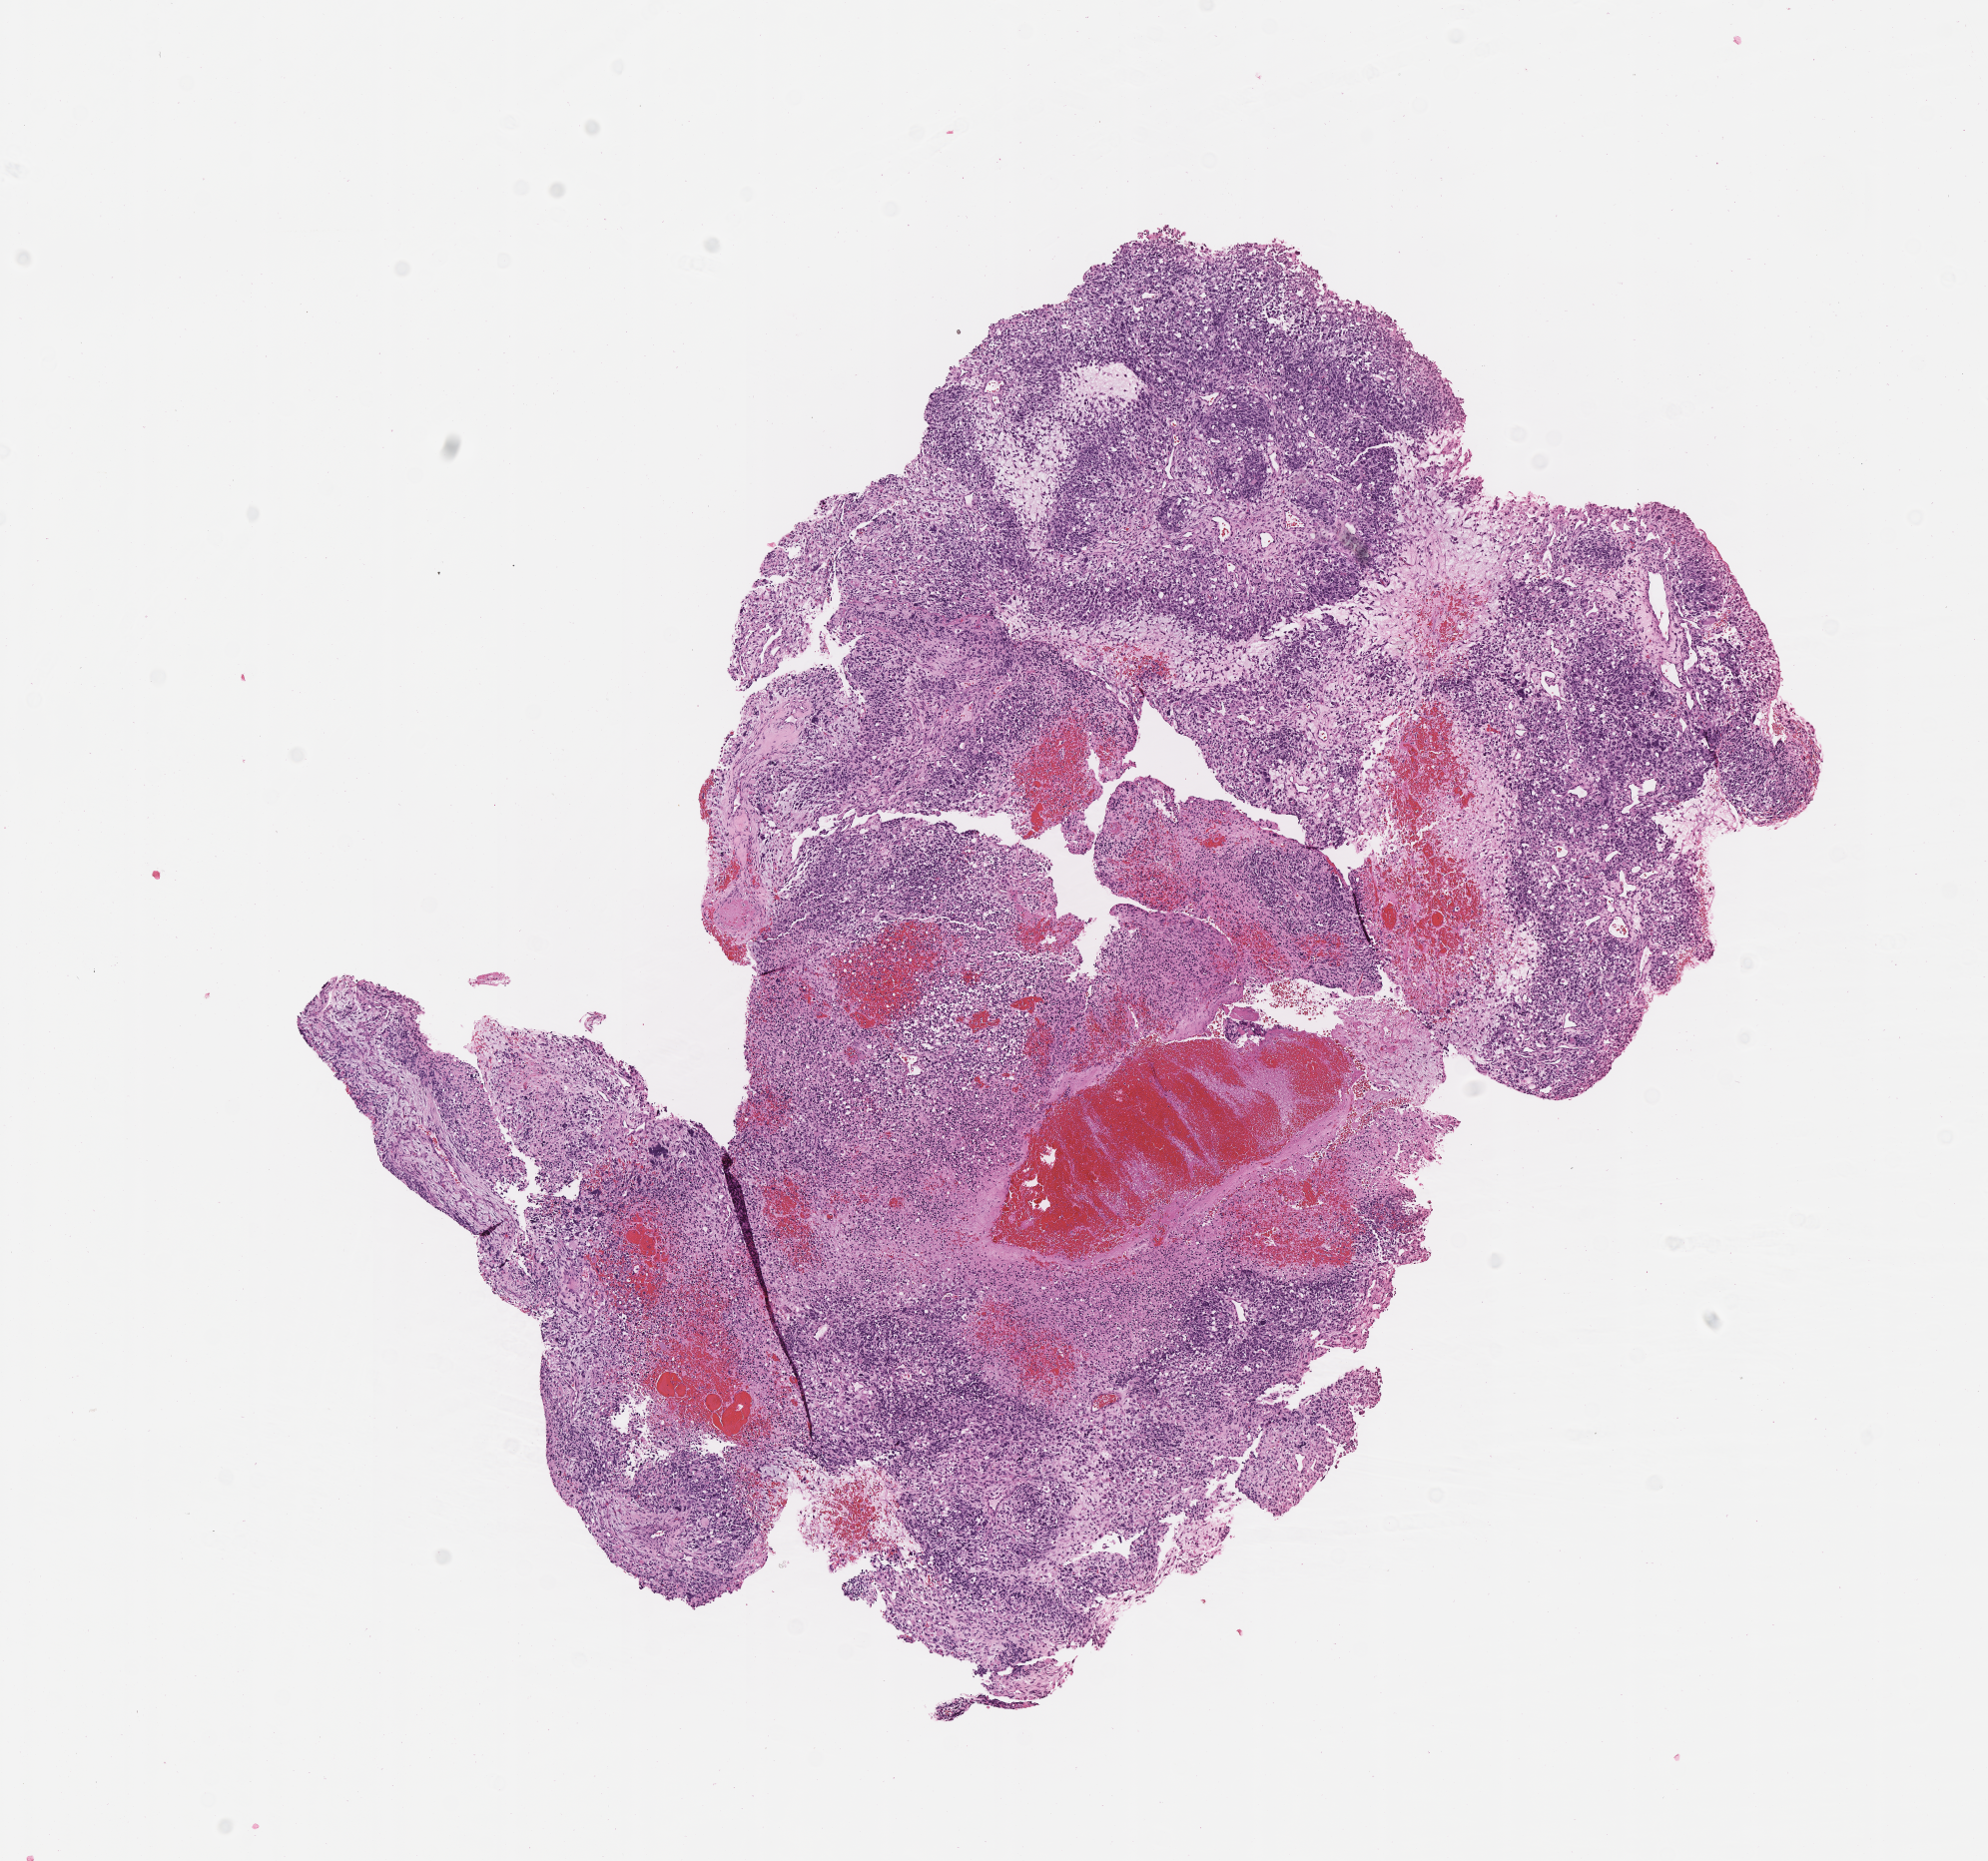
Whole-slide image, haematoxylin and eosin stain of tumor tissue, whole scanned area (about 8.1 x 7.5 mm) shown as a low-resolution overview, formalin-fixed, paraffin-embedded (FFPE) tissue, sample anatomic site: pelvis. Patient: male, age 7.4 years at diagnosis.
Metastatic status at presentation (as recorded): metastatic (confirmed). Stage (as recorded): 4. Diagnosis: rhabdomyosarcoma; histological classification: embryonal rhabdomyosarcoma.